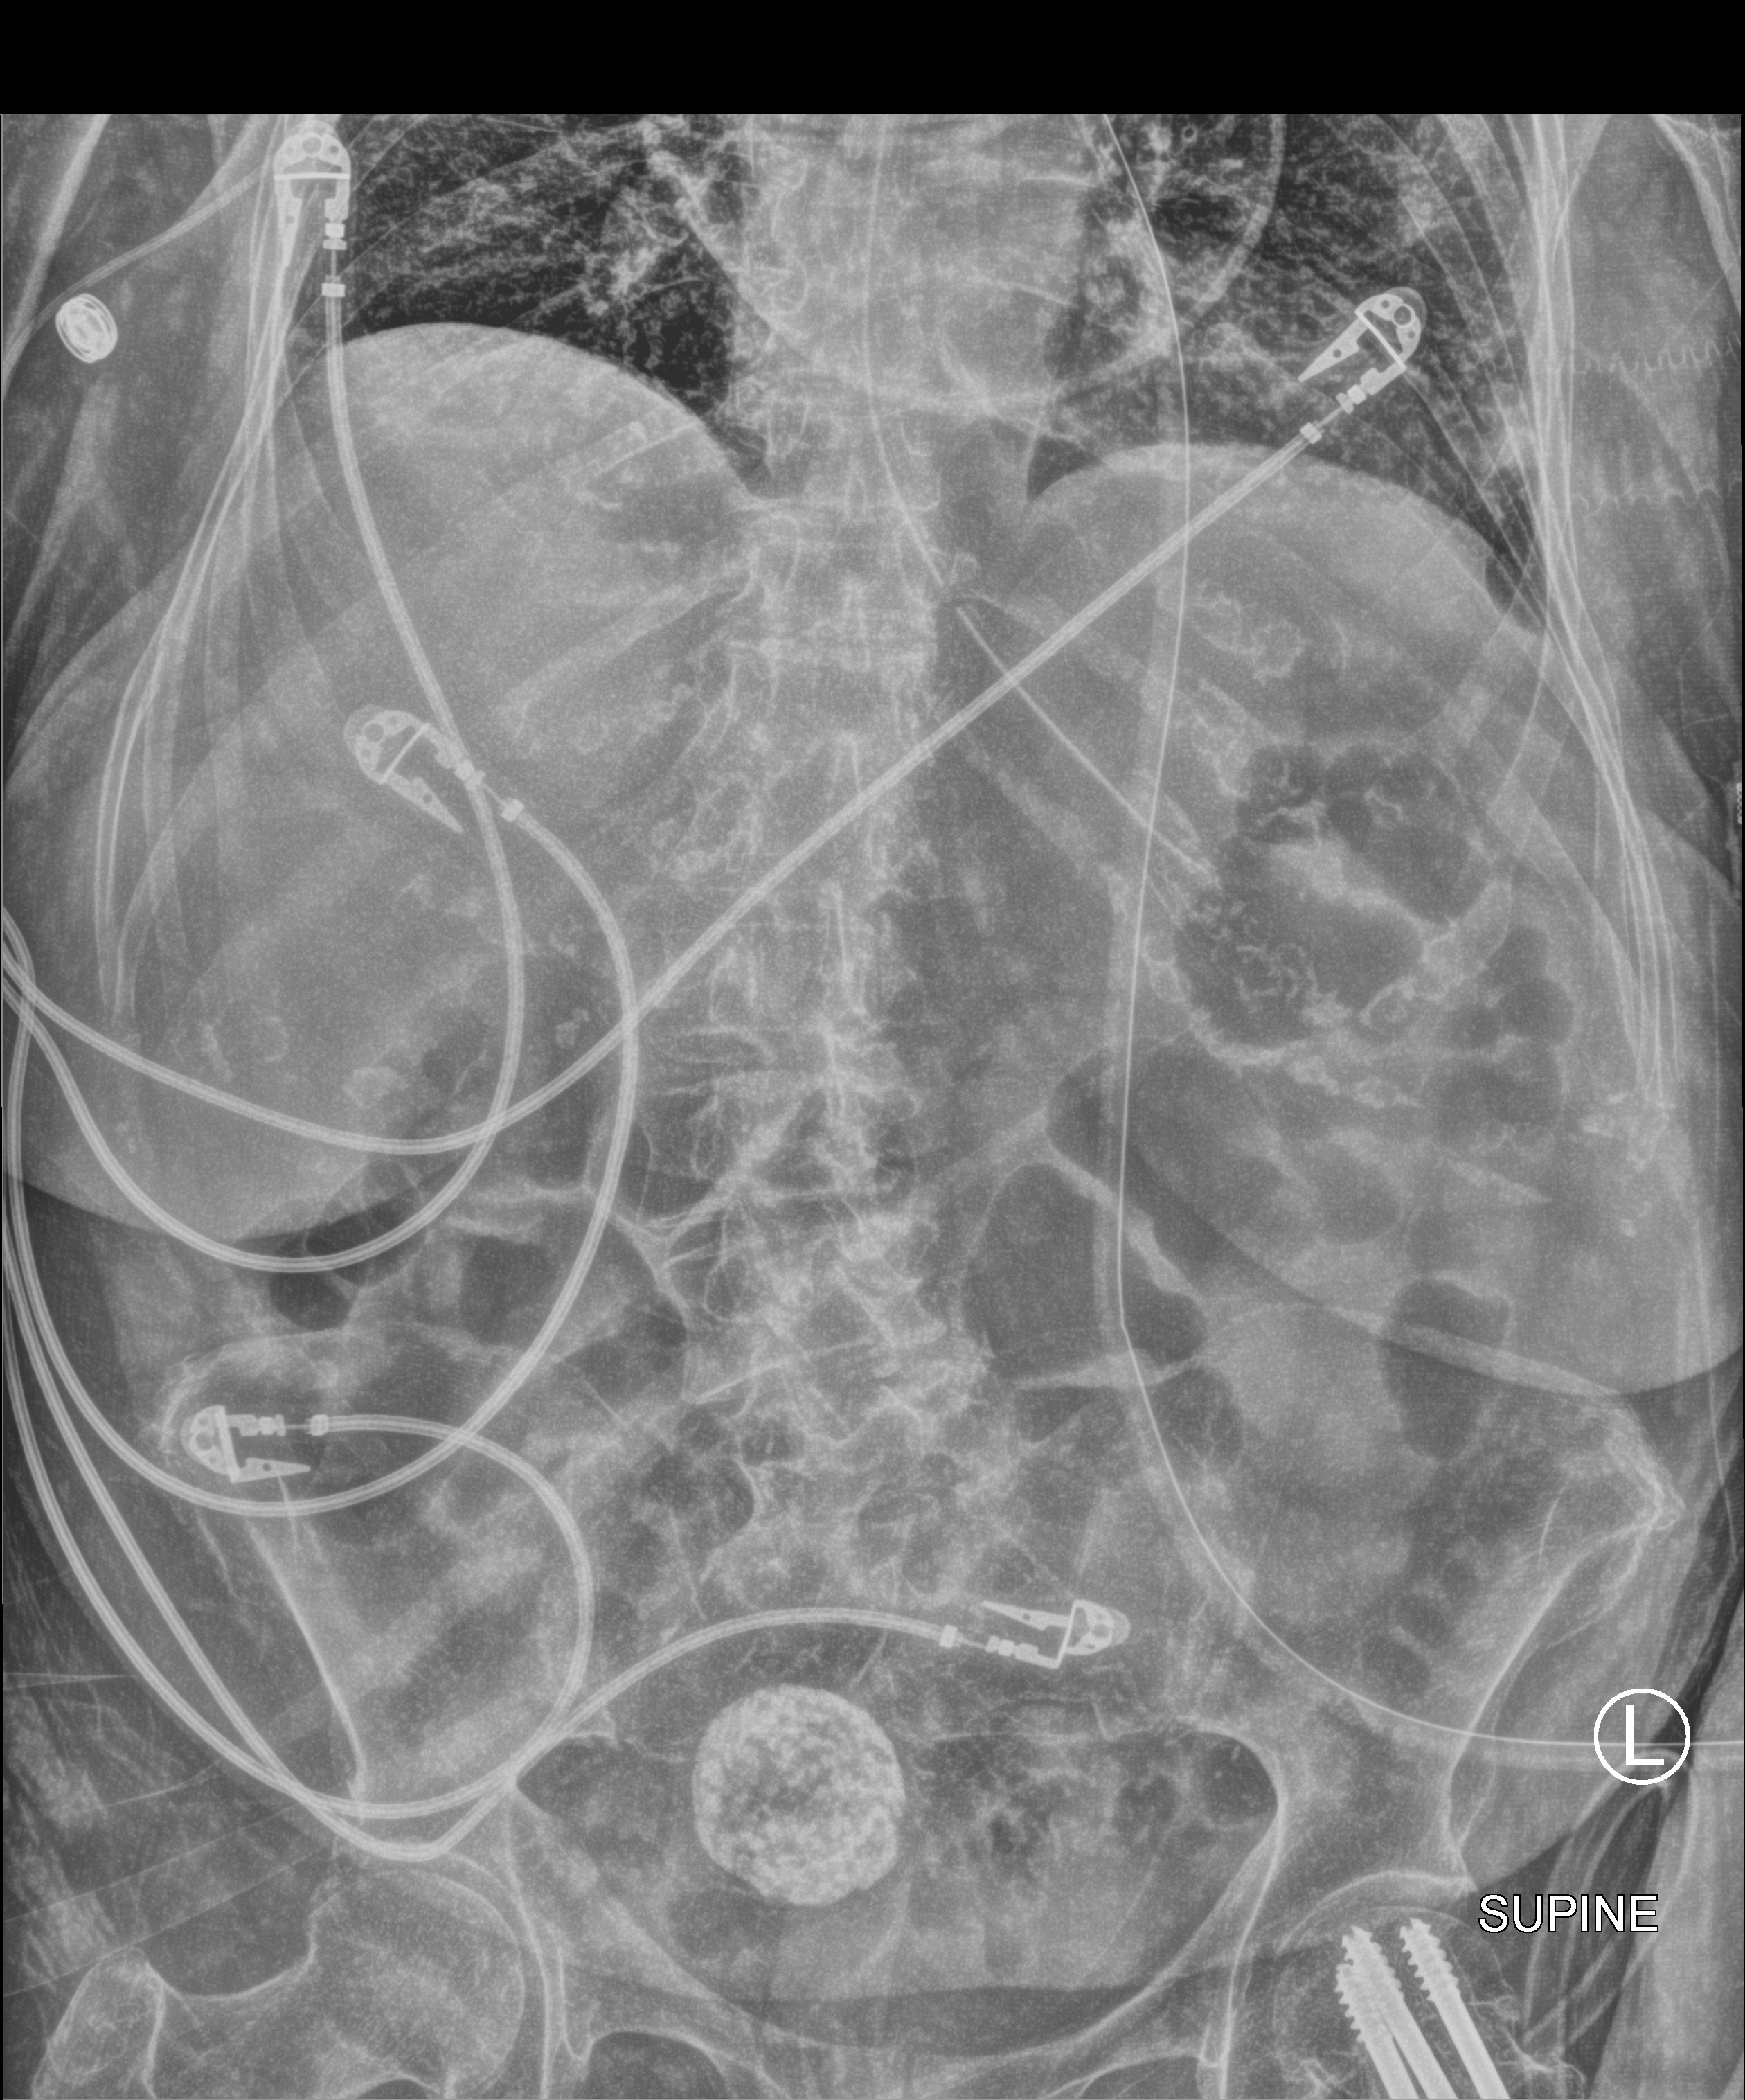
Bedside abdomen radiograph (computed radiography); anteroposterior (AP) projection. Female patient hospitalised with COVID-19, age 75–90 years.
Admission-level facts for this patient (not findings on this image; timing relative to this image not recorded): admitted to intensive care during this hospital stay: yes; chronic kidney disease (admission record): yes.